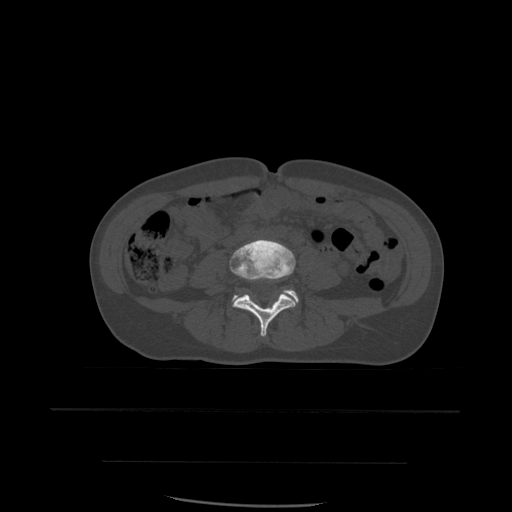
CT including the spine, one axial slice; slice 165 of 574 in the series (ordered by position); bone window (W 1800 / L 400 HU); 1.25 mm slice thickness; 512 × 512 image matrix, field of view 392 × 392 mm. Patient age 48 years. From the clinical record (not read from this slice): primary cancer: lung; vertebrae with lytic lesions (as recorded): T11.
Outlined on this slice (semi-automatic segmentation, software-assisted and operator-edited):
- L4 vertebra: bounding box (x1, y1, x2, y2) in pixels: (230, 240, 296, 337)
- L5 vertebra: (233, 290, 299, 308)